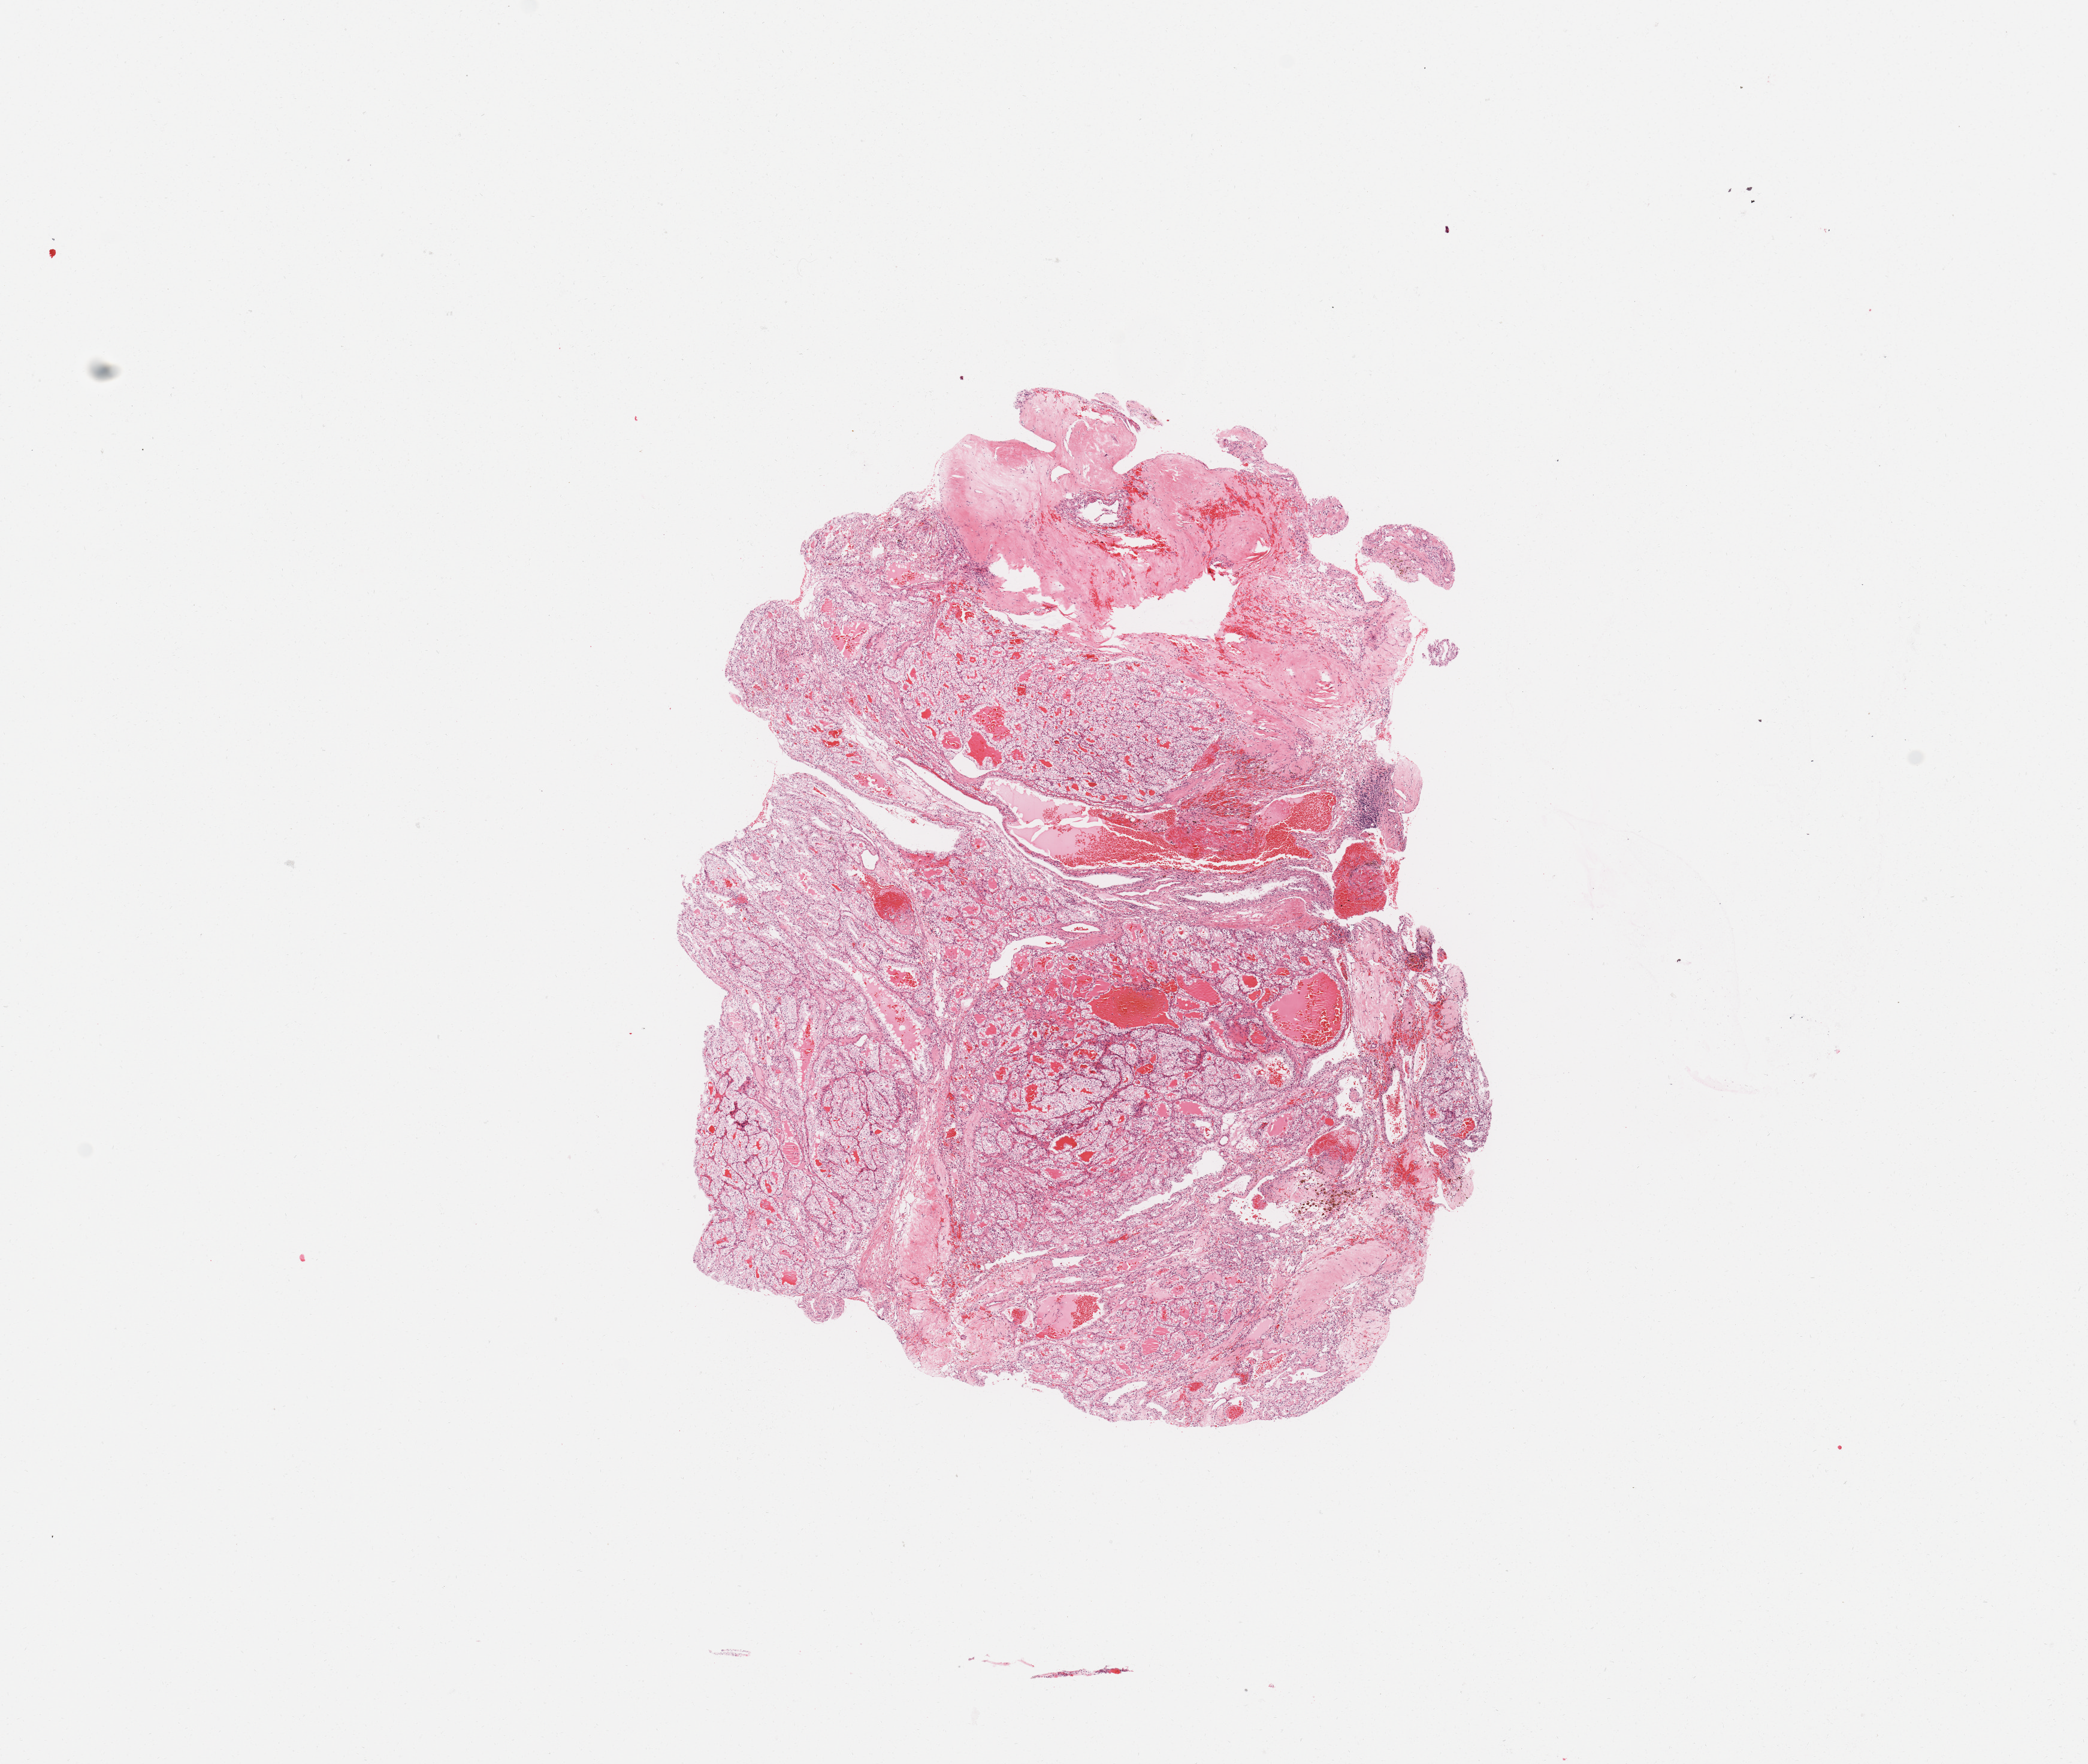
H&E whole-slide image, a low-resolution overview of the entire scanned area, about 13.8 x 11.6 mm (slide scanned at 20x), tumour tissue sample, sampled site: kidney. 31-year-old male patient. Histologic grade: G2 (moderately differentiated). Pathologist review of this section (percent, as recorded): tumour nuclei 80%, necrosis 5%.
AJCC pathologic stage: I. Histologic diagnosis: Renal cell carcinoma, NOS. Primary tumour site (as recorded): lower pole.